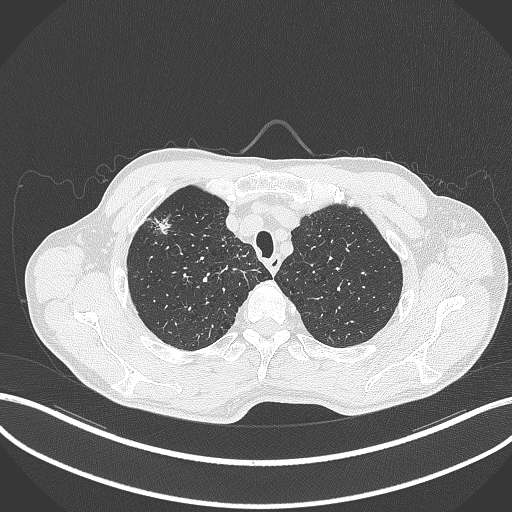
Chest CT, one axial slice. Position 355 of 427 along the scan axis. Lung window (W 1500 / L -600 HU). 1 mm slice thickness. 512 × 512 image matrix, field of view 400 × 400 mm. Patient: male, 69 years. Case-level facts recorded for this patient, not image findings: clinical TNM (as recorded): T1b N1 M0.
Annotated regions visible in this slice (bounding box drawn by a radiologist):
- lung tumour (recorded histology: adenocarcinoma): box from (x=147, y=212) to (x=180, y=239) px